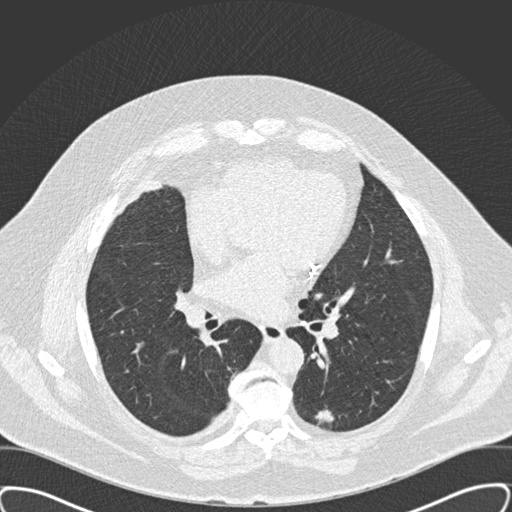
Low-dose screening chest CT, one axial slice; position 88 of 159 along the scan axis; reconstruction kernel B30f; lung window (W 1500 / L -600 HU); 2 mm slice thickness; 512 × 512 image matrix, field of view 400 × 400 mm.
Outlined on this slice (outlined manually by an expert reader):
- lesion 1 (tumor, lower lobe of left lung): bounding box [x1, y1, x2, y2] px = [316, 410, 334, 422]